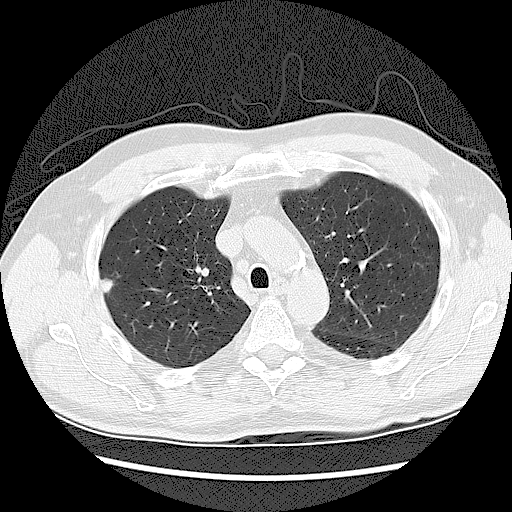
Low-dose screening chest CT, one axial slice; slice 86 of 120 in the series (ordered by position); reconstruction kernel LUNG; 120 kVp; lung window (W 1500 / L -600 HU); 2.5 mm slice thickness; 512 × 512 image matrix, field of view 360 × 360 mm.
Structures marked on this image (manually delineated by an expert):
- lesion 1 (tumor, upper lobe of right lung): bounding box (x1, y1, x2, y2) in pixels: (101, 278, 115, 296)